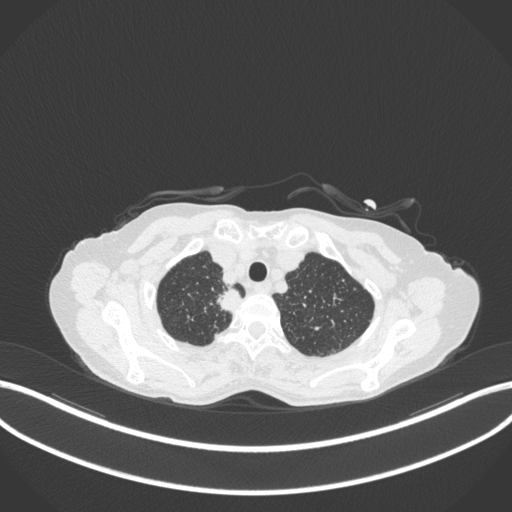
Chest CT, one axial slice; position 325 of 363 along the scan axis; reconstruction kernel B31f; 120 kVp; lung window (W 1500 / L -600 HU); 1 mm slice thickness; 512 × 512 image matrix, field of view 400 × 400 mm. Patient: female, 75 years. Case-level facts recorded for this patient, not image findings: clinical TNM (as recorded): T1c N1 M1.
Annotated regions visible in this slice (bounding box drawn by a radiologist):
- lung tumour (recorded histology: adenocarcinoma): box from (x=210, y=284) to (x=244, y=319) px